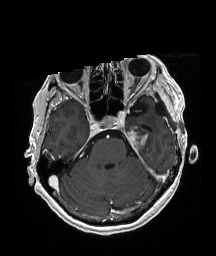
Brain MRI from a brain-tumour surgery series, one axial slice. Slice 132 of 192 in the series (ordered by position). T1-weighted post-contrast. 216 × 256 image matrix, field of view 211 × 250 mm. Case-level facts recorded for this patient, not image findings: histopathology: Glioblastoma; WHO grade: 4; IDH mutation: no; tumour location: Left Temporal.
Annotated regions visible in this slice (expert manual segmentation):
- previous resection cavity: box from (x=156, y=106) to (x=162, y=113) px